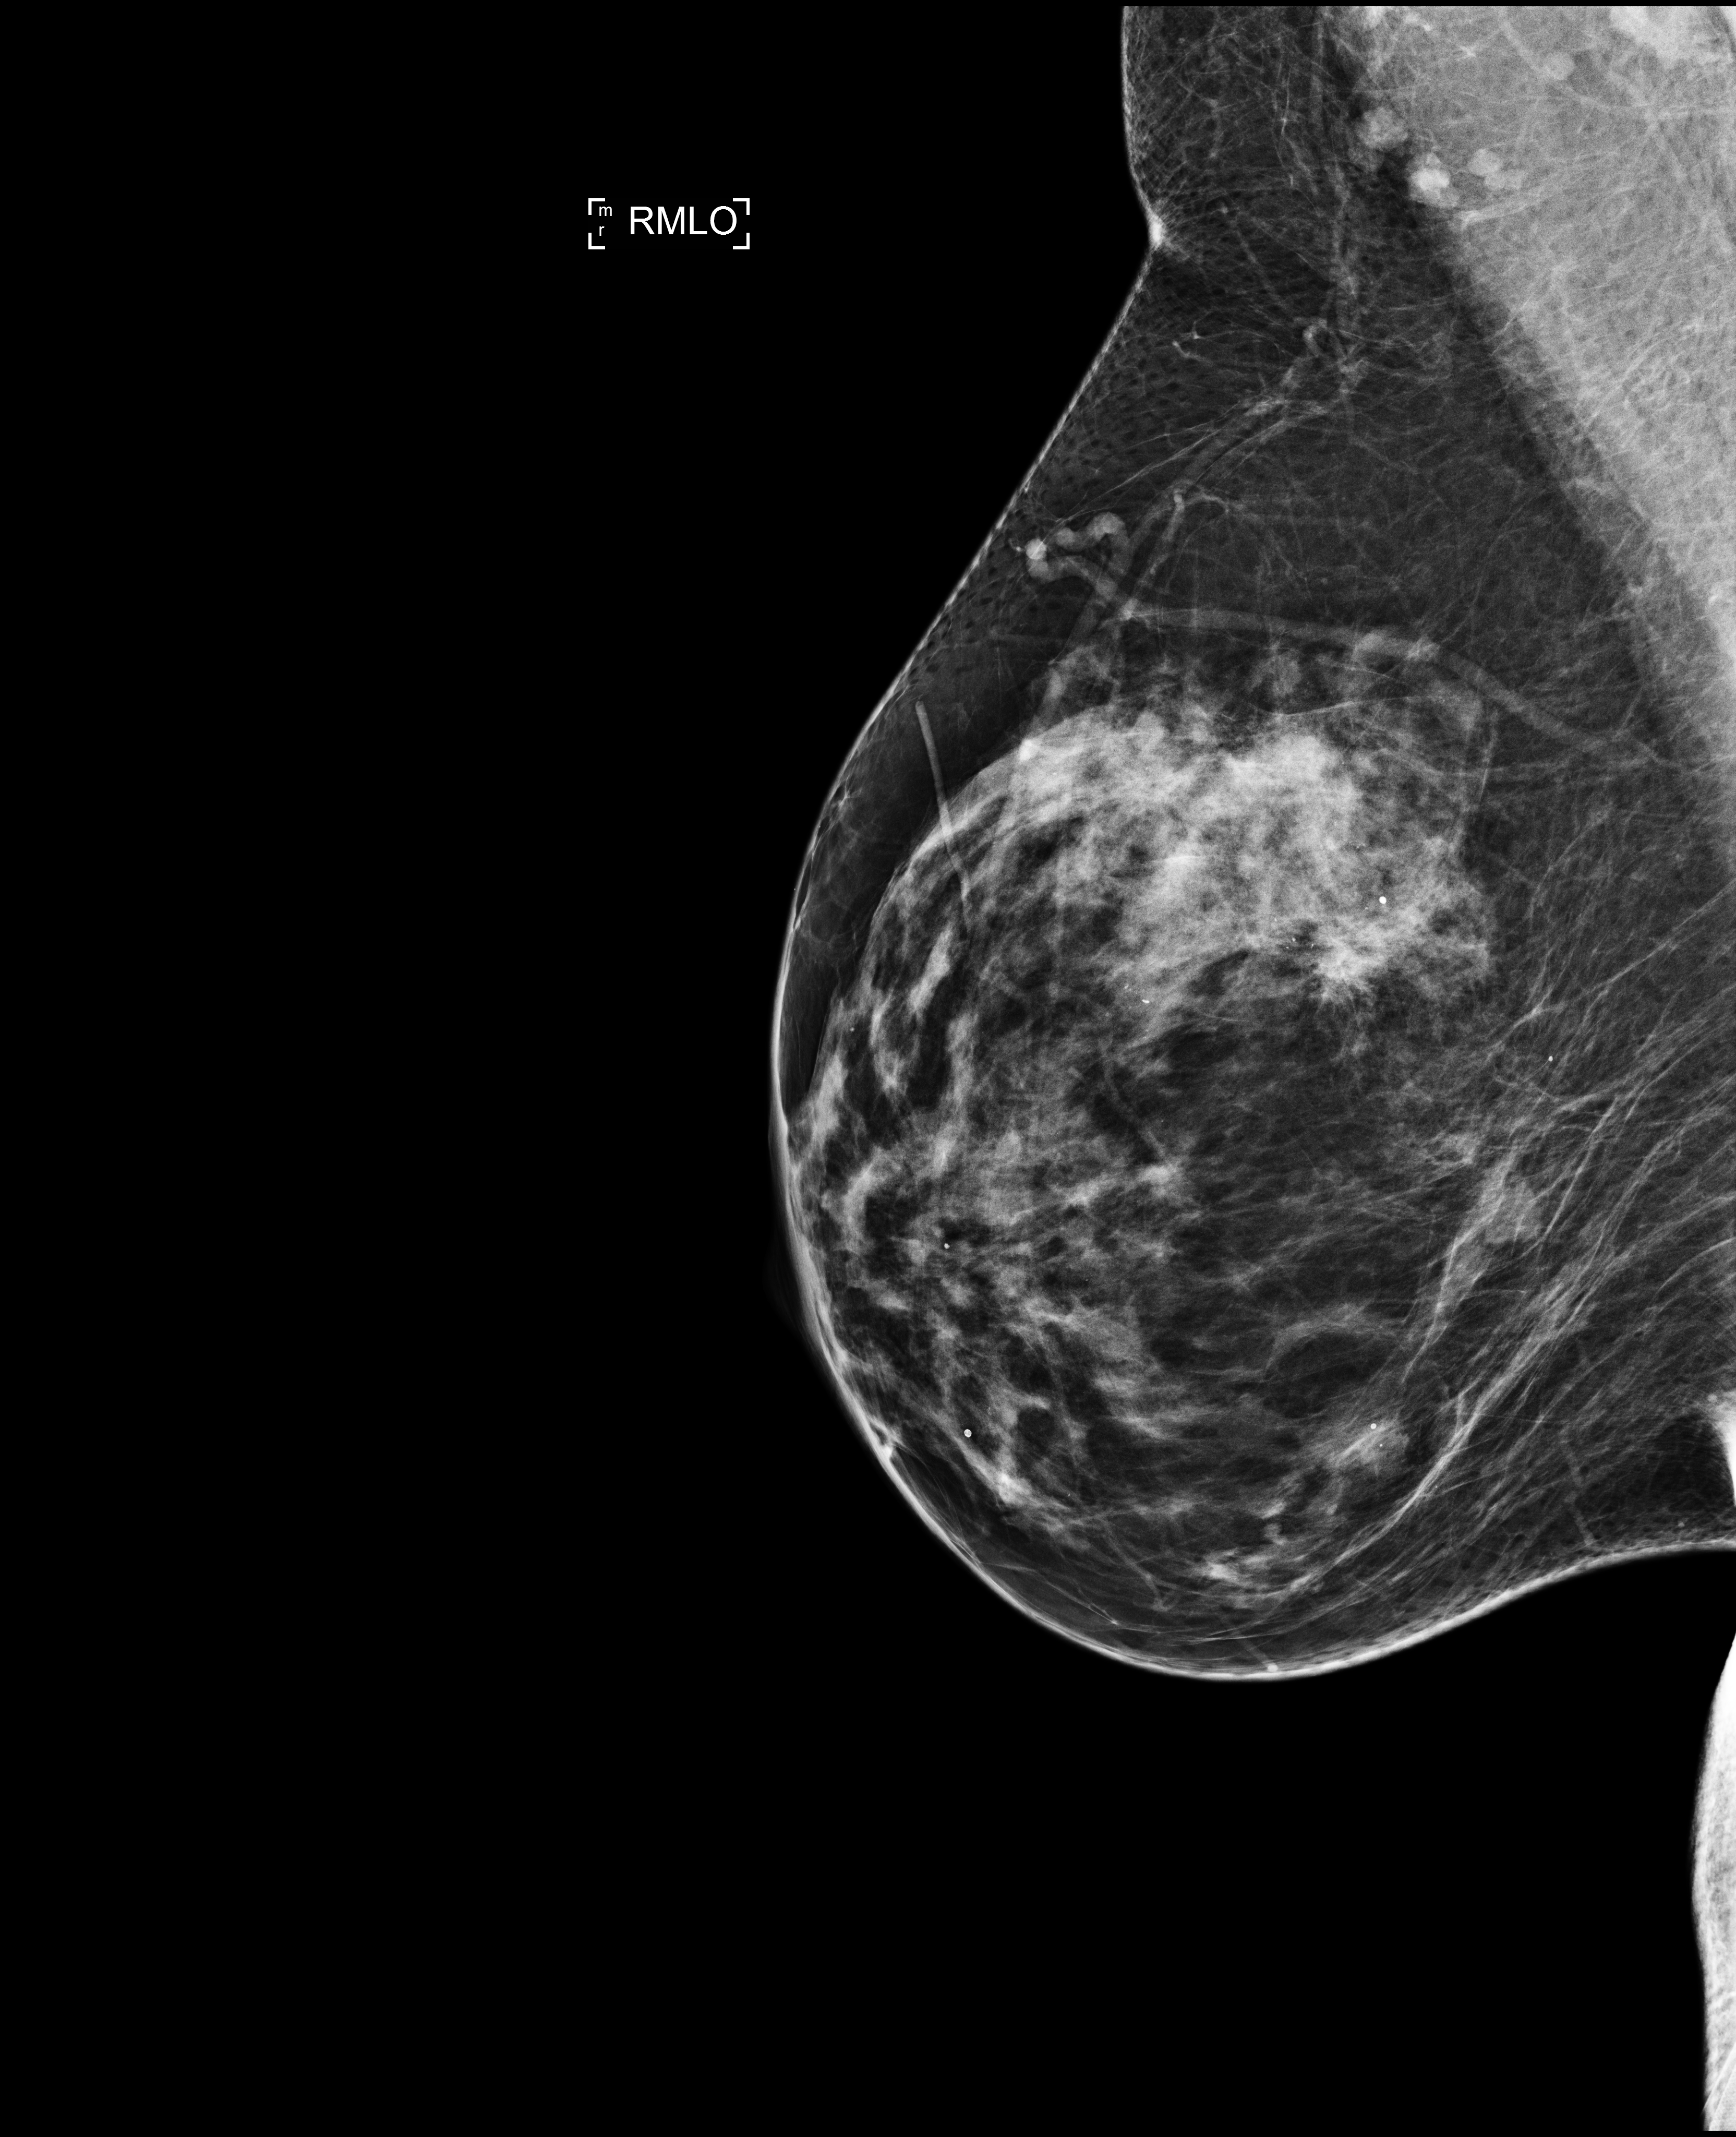
Digital mammogram (FFDM); right breast; mediolateral oblique (MLO) view; annual screening mammography examination; compressed breast thickness 70 mm; system: Selenia Dimensions. Female patient, age 59 years.
Breast density at the screening exam (both breasts): heterogeneously dense (BI-RADS density category c). Final BI-RADS assessment for this screening round (tomosynthesis exam, both breasts): category 2. Recall: no recall after this screen.